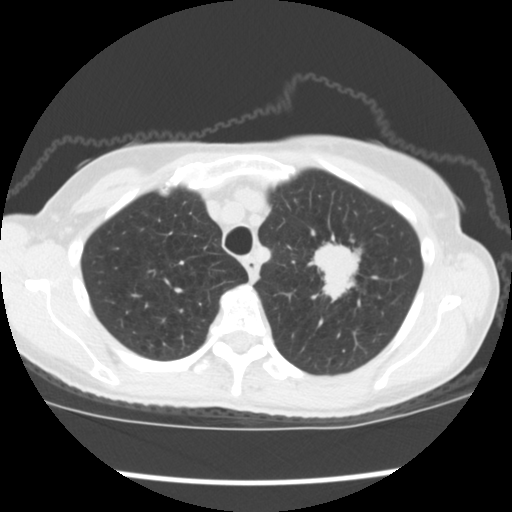
Low-dose screening chest CT, one axial slice; position 147 of 176 along the scan axis; lung window (W 1500 / L -600 HU); 2.5 mm slice thickness; 512 × 512 image matrix.
Annotated regions visible in this slice (expert manual segmentation):
- lesion 1 (tumor, upper lobe of left lung): box from (x=310, y=237) to (x=362, y=301) px